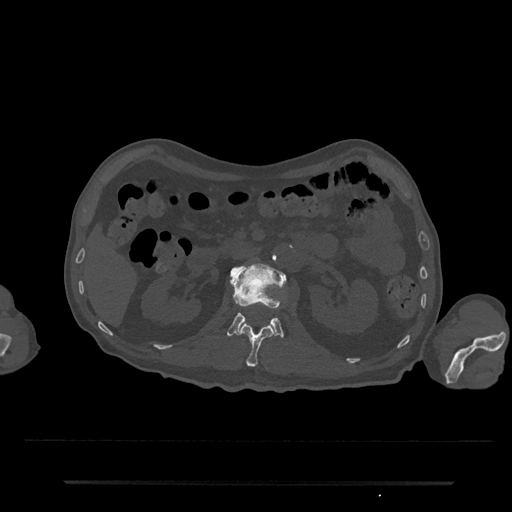
CT including the spine, one axial slice. Slice 97 of 797 in the series (ordered by position). Reconstruction kernel Br40s/3. 120 kVp. Bone window (W 1800 / L 400 HU). 512 × 512 image matrix, field of view 427 × 427 mm. Male patient, age 74 years. Case-level facts recorded for this patient, not image findings: primary cancer: prostate.
Structures marked on this image (semi-automatic segmentation, software-assisted and operator-edited):
- L1 vertebra: box from (x=237, y=322) to (x=275, y=367) px
- L2 vertebra: (x=227, y=263)–(x=286, y=337)